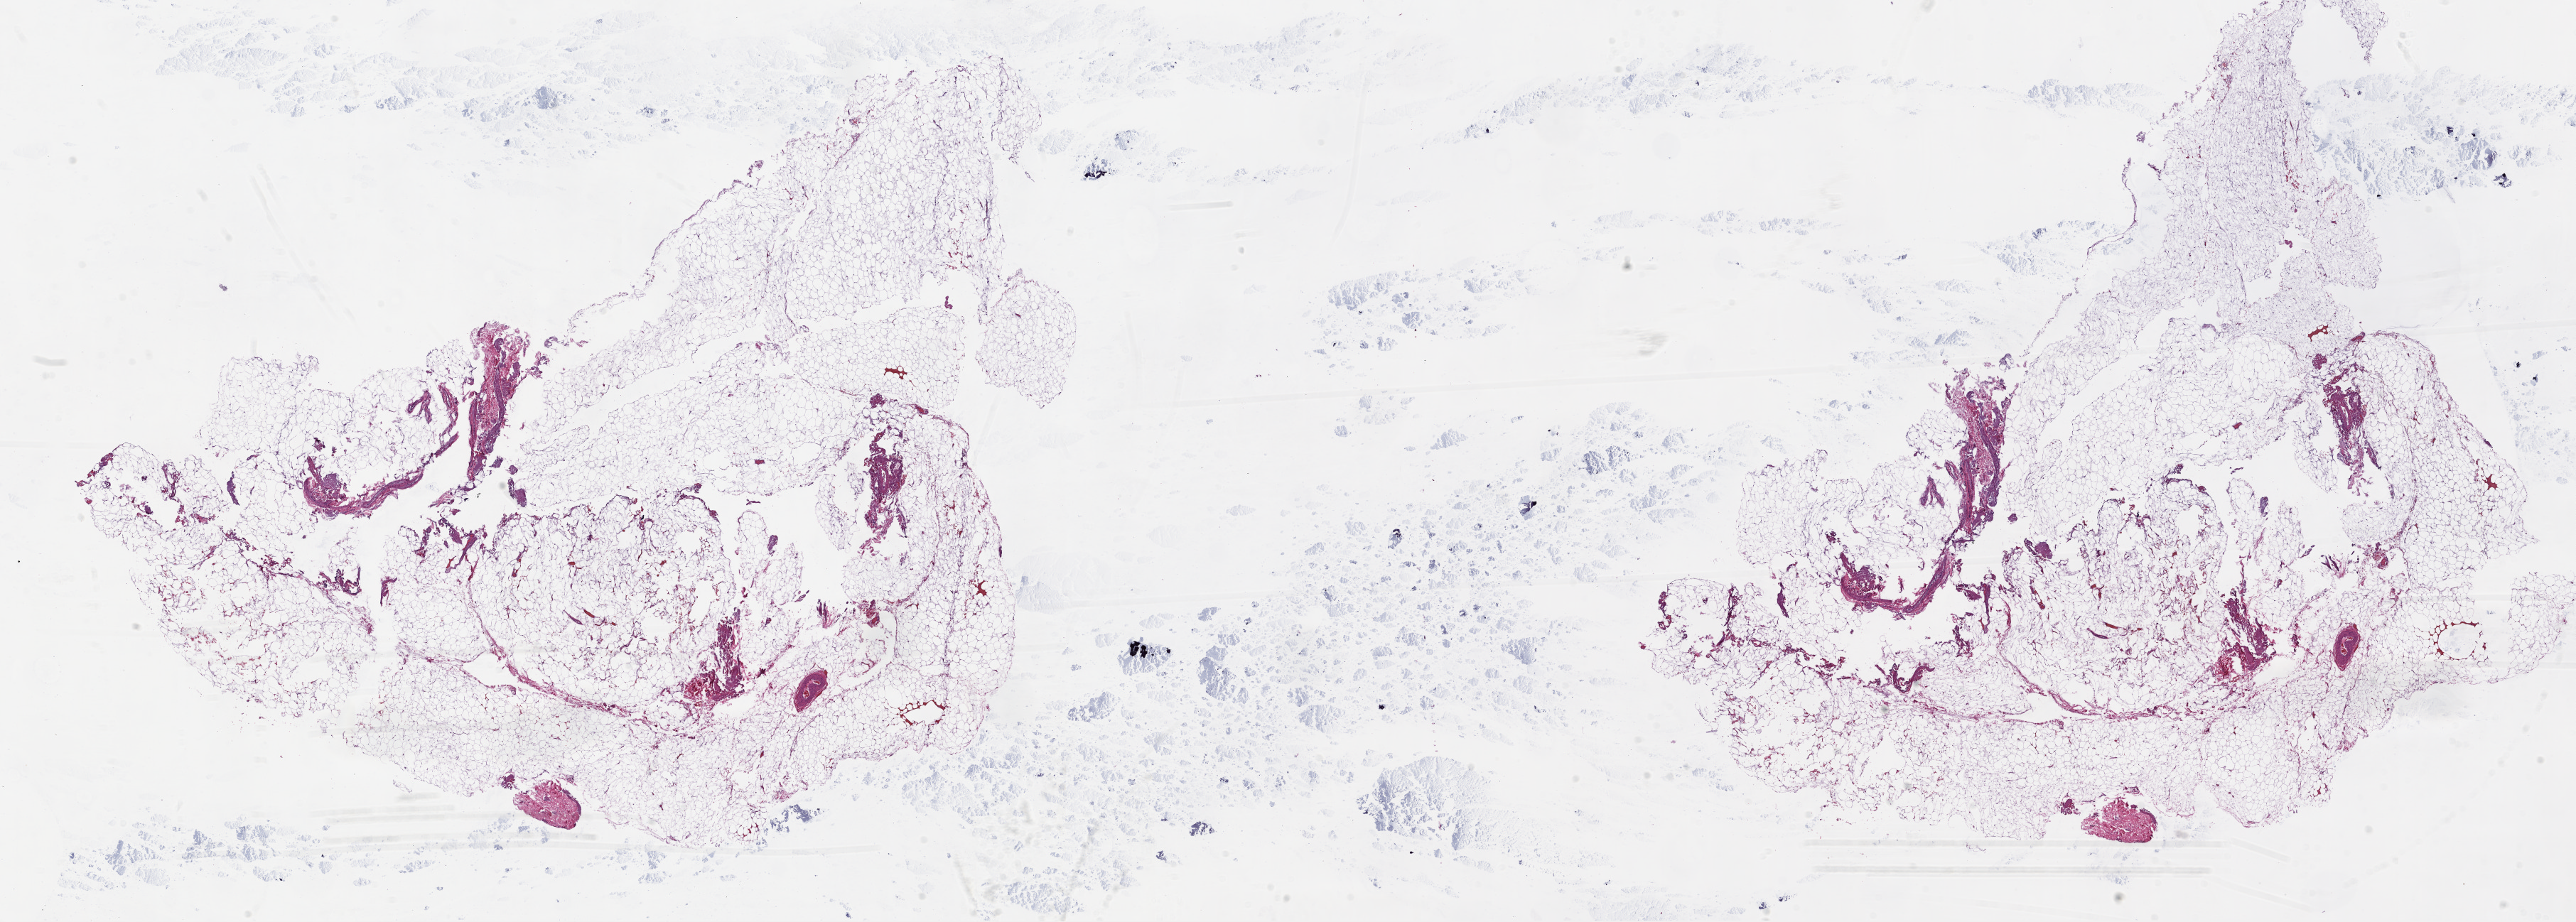
Whole-slide histology image, Hematoxylin and eosin (H&E) stained — low-resolution overview of the scanned area, about 29.1 x 10.4 mm. Frozen section from the top of the tissue portion. Sample: solid tissue normal (non-tumour tissue), kidney. Patient: female, age at initial diagnosis 59 years.
• this section: solid tissue normal (non-tumour) sample from the same patient
• patient diagnosis: Papillary adenocarcinoma, NOS